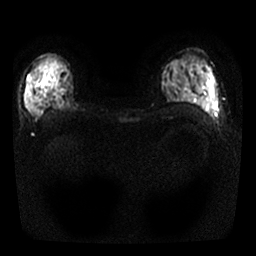
Breast MRI, one axial slice. Diffusion-weighted series; image 2 of 4 stored at this slice position (different b-values; order by instance number). 1.5 T. 256 × 256 image matrix, field of view 300 × 300 mm. Female patient.
Annotated regions visible in this slice (expert manual segmentation):
- tumour on diffusion-weighted imaging: box from (x=25, y=100) to (x=33, y=114) px